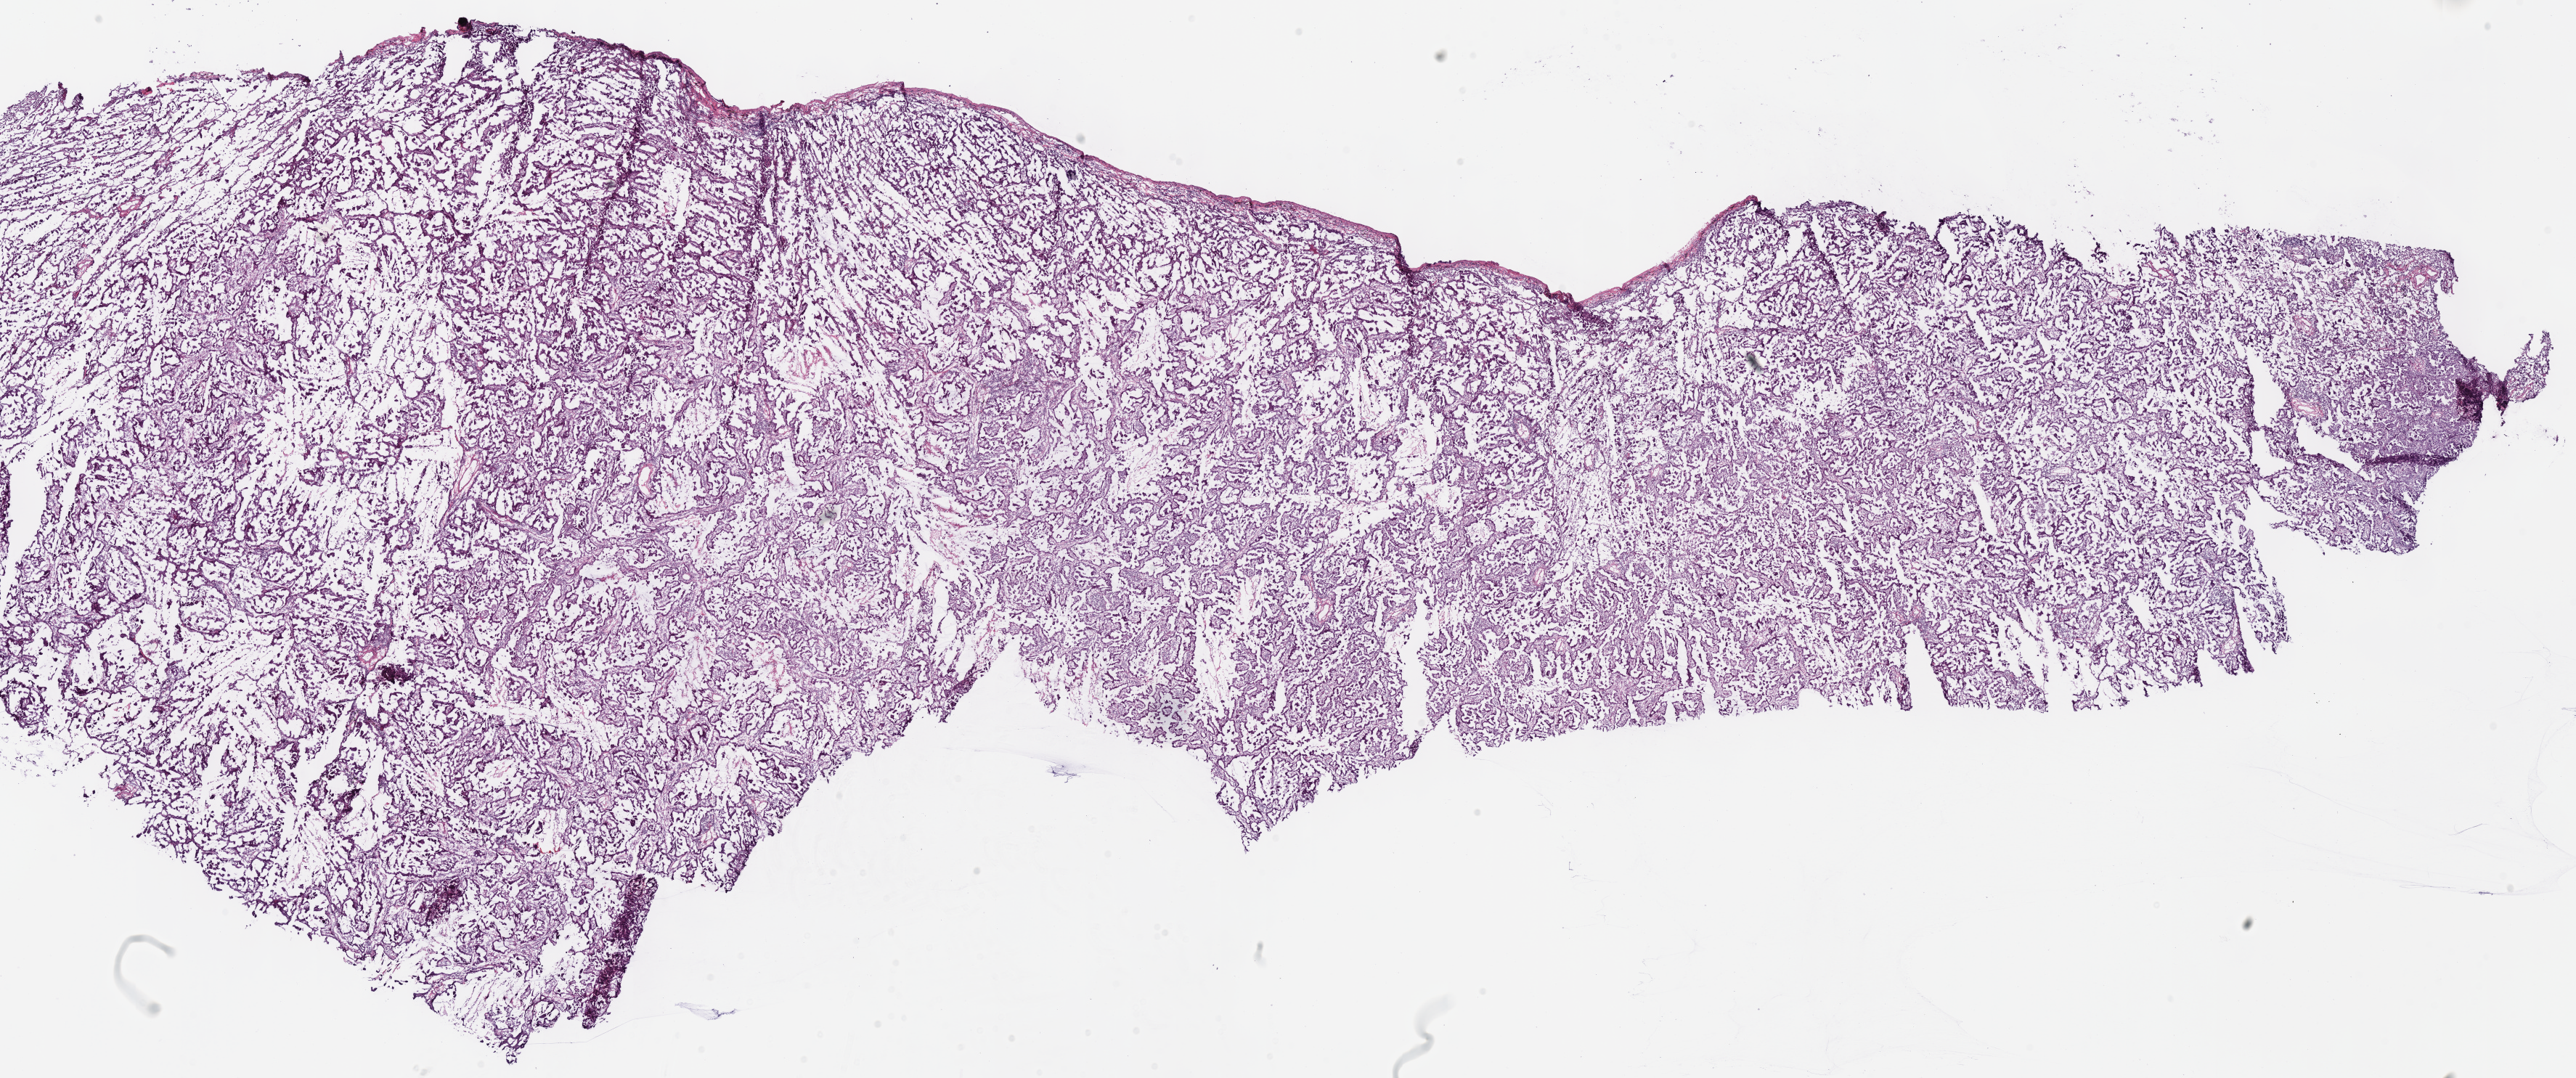
Whole-slide histology image, H&E — shown as a low-resolution overview of the whole scanned area (about 27.9 x 11.7 mm, from a 40x scan), frozen section from the bottom of the tissue portion, lung, primary tumour sample. Male patient; age at initial diagnosis 70 years. Composition of this section per pathologist review: tumour cells 100%, tumour nuclei 70%, normal cells 0%, stromal cells 0%, necrosis 0%. Infiltration values recorded for this section: lymphocyte infiltration 20%, monocyte infiltration 0%, neutrophil infiltration 0%.
* TNM: T2b N0 M0
* AJCC pathologic stage: IIA
* diagnosis: Adenocarcinoma, NOS (middle lobe, lung)